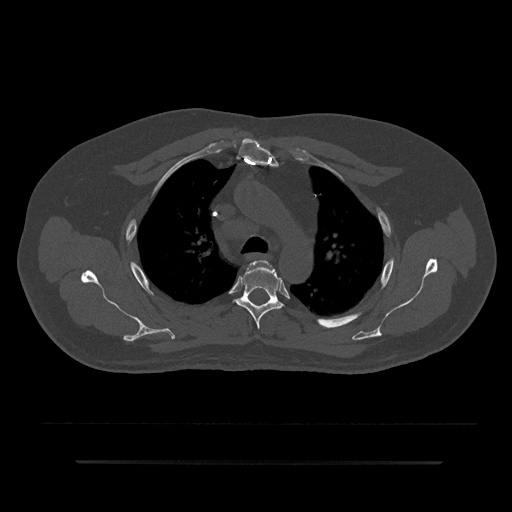
CT including the spine, one axial slice; slice 618 of 797 in the series (ordered by position); 120 kVp; bone window (W 1800 / L 400 HU); 0.5 mm slice thickness; 512 × 512 image matrix. Male patient, age 59 years. From the clinical record (not read from this slice): primary cancer: bile ducts.
Outlined on this slice (semi-automatically segmented with operator editing):
- T3 vertebra: bounding box <254,261,275,271> (left, top, right, bottom; pixels)
- T4 vertebra: <234,261,283,329>